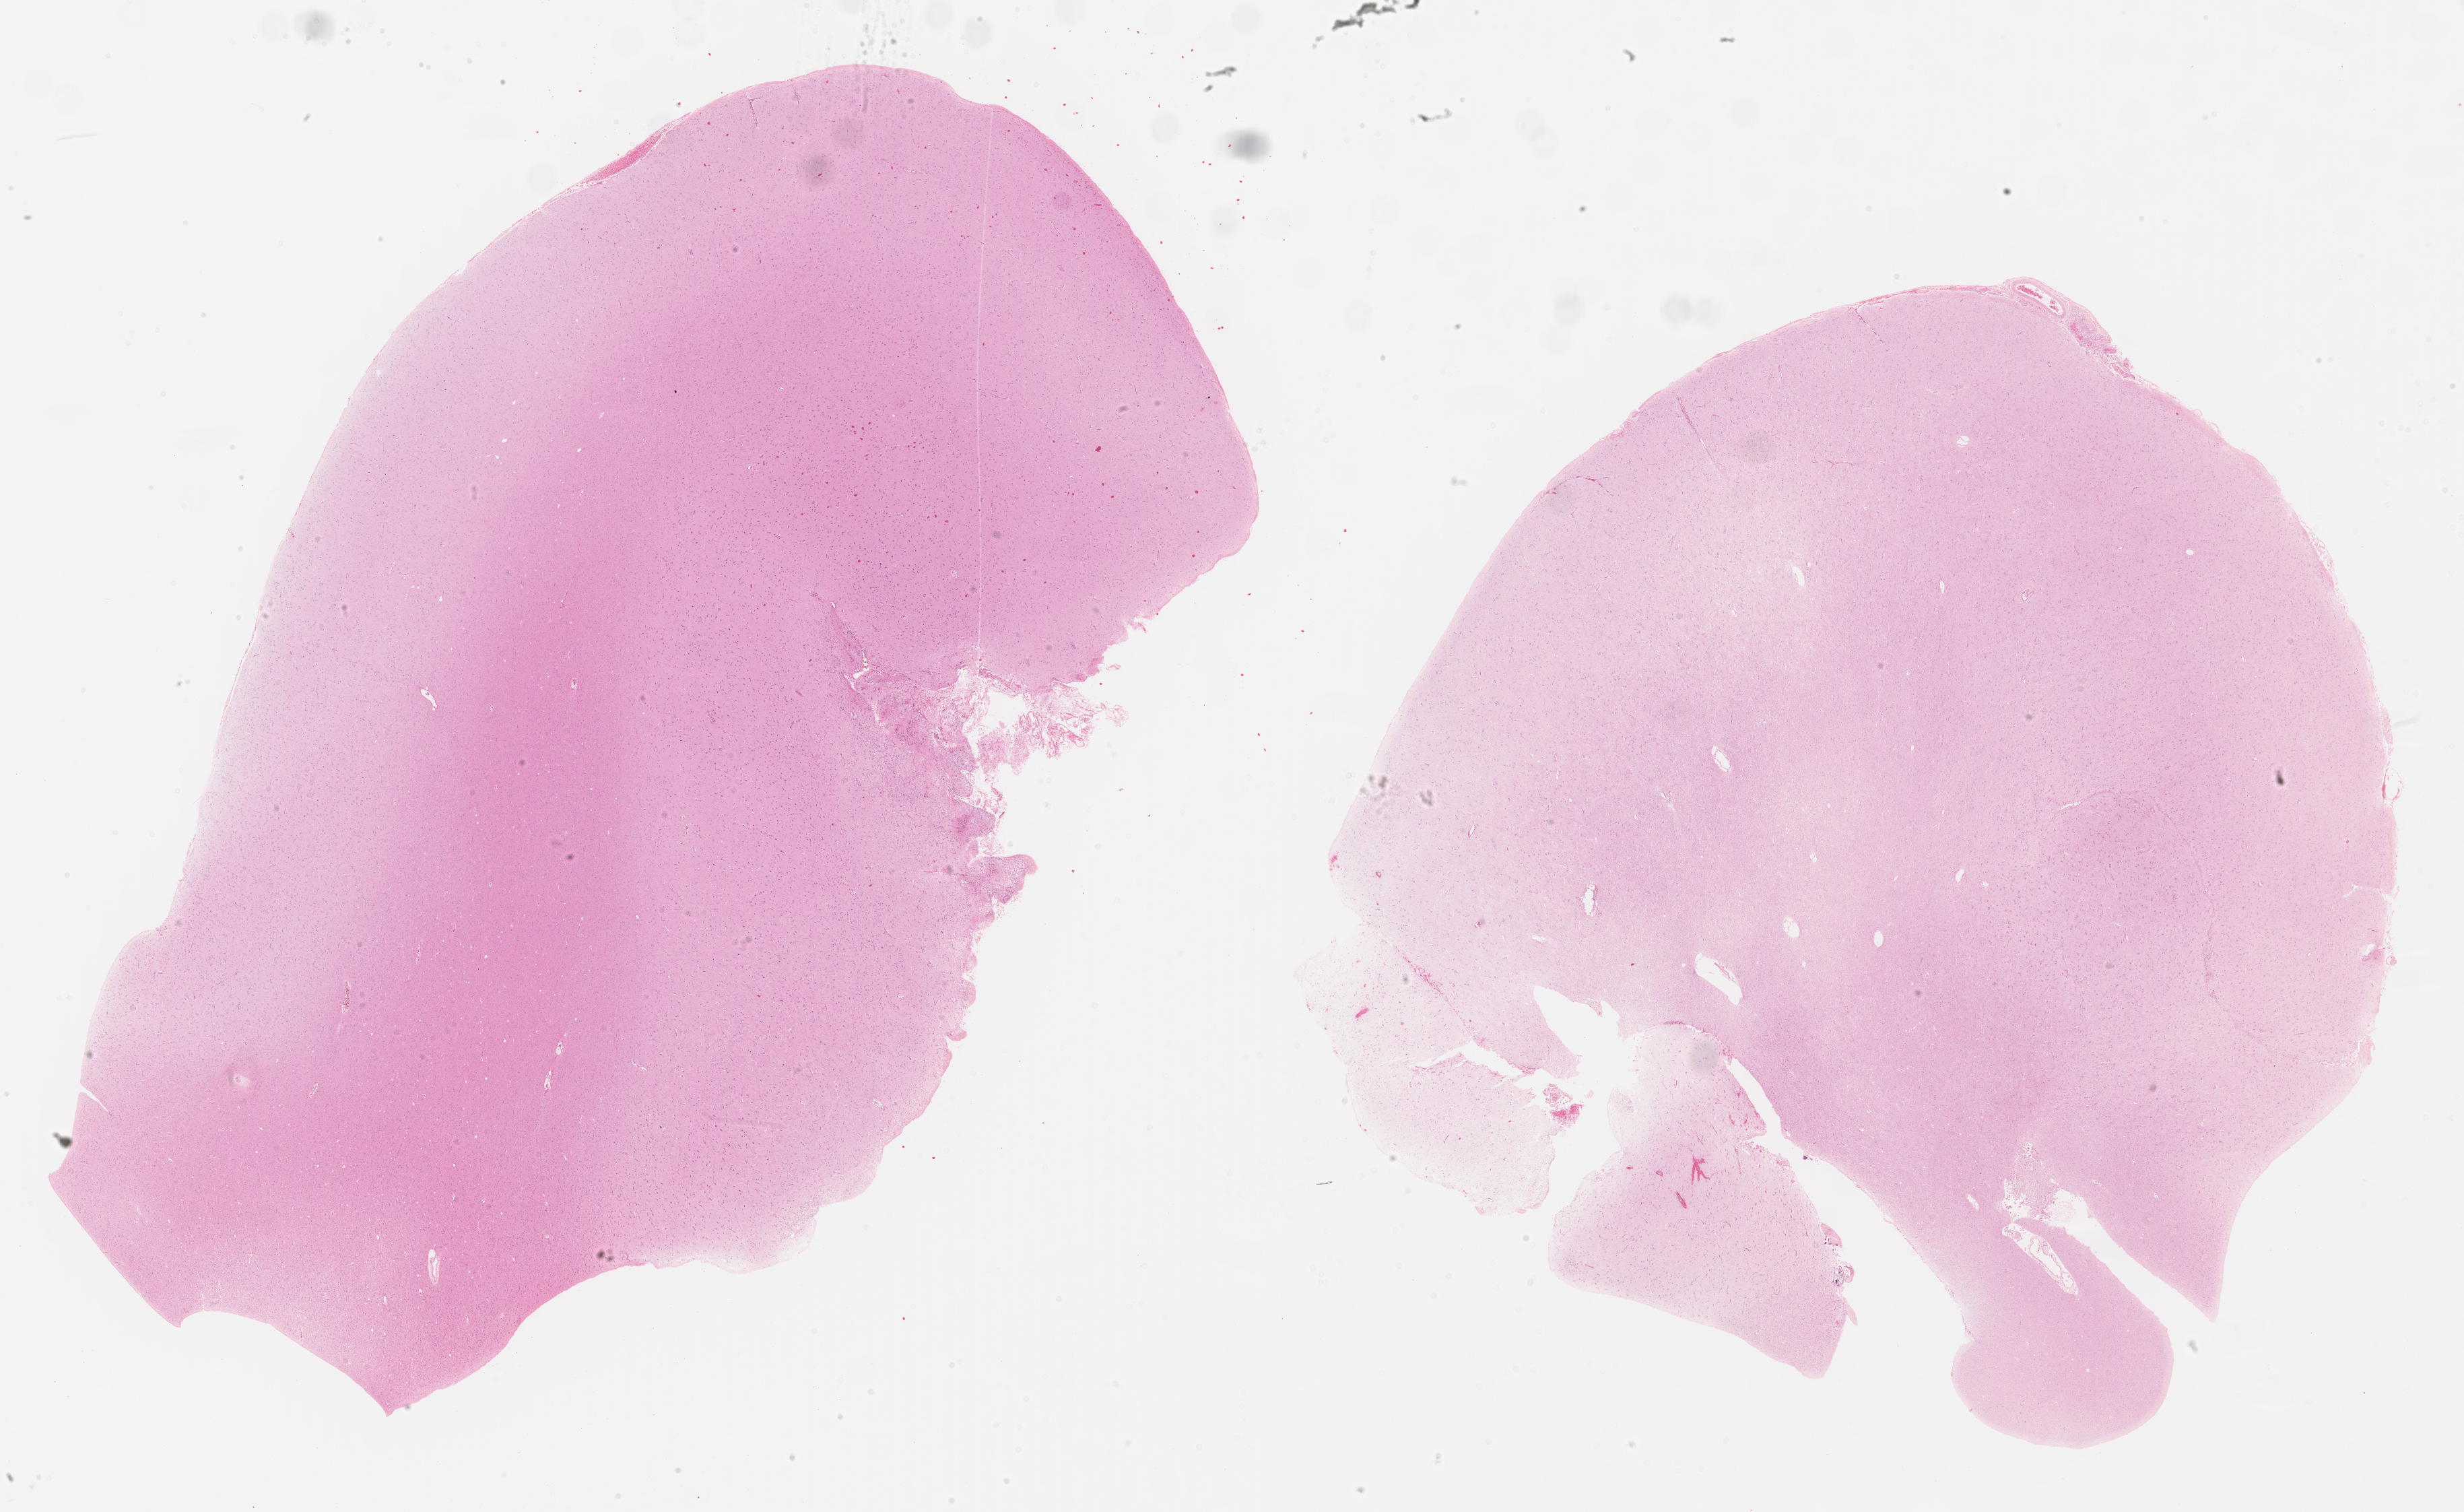
Digitized H&E tissue section (whole slide), shown as a low-resolution overview of the whole scanned area (about 29.5 x 18.1 mm, acquisition: 40x scan); formalin-fixed paraffin-embedded (FFPE) diagnostic section; sample: primary tumour, brain. Patient: male, age at initial diagnosis 40 years. Histologic grade: G2 (moderately differentiated).
* diagnosis: Oligodendroglioma, NOS
* laterality: right